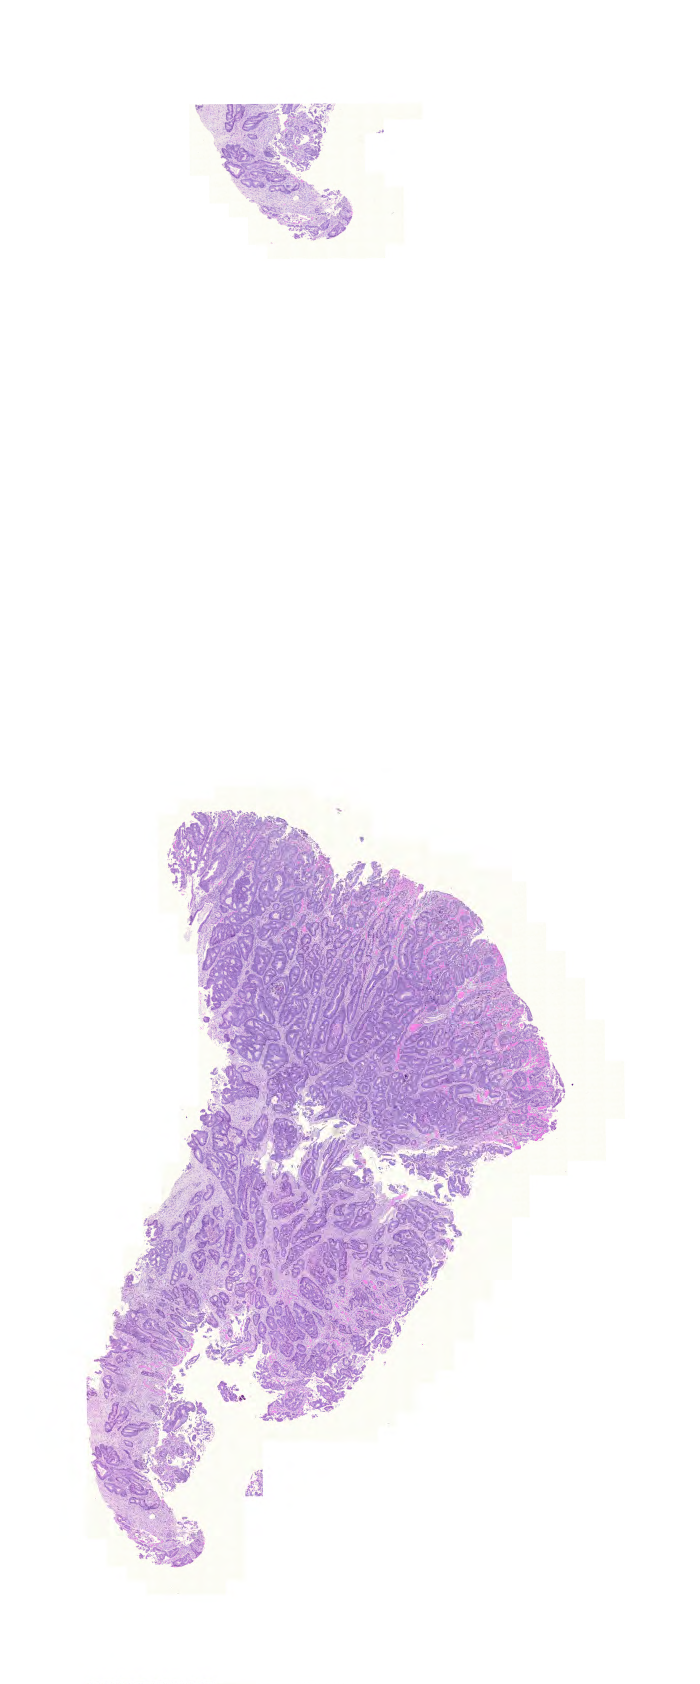
Digitized H&E tissue section (whole slide) — a low-resolution overview of the entire scanned area, about 10.4 x 25.1 mm (slide scanned at 20x). FFPE section. Sample: primary tumour, rectum. Female, age 84 years at initial diagnosis.
AJCC pathologic stage: I (6th edition). Diagnosis: Adenocarcinoma, NOS.